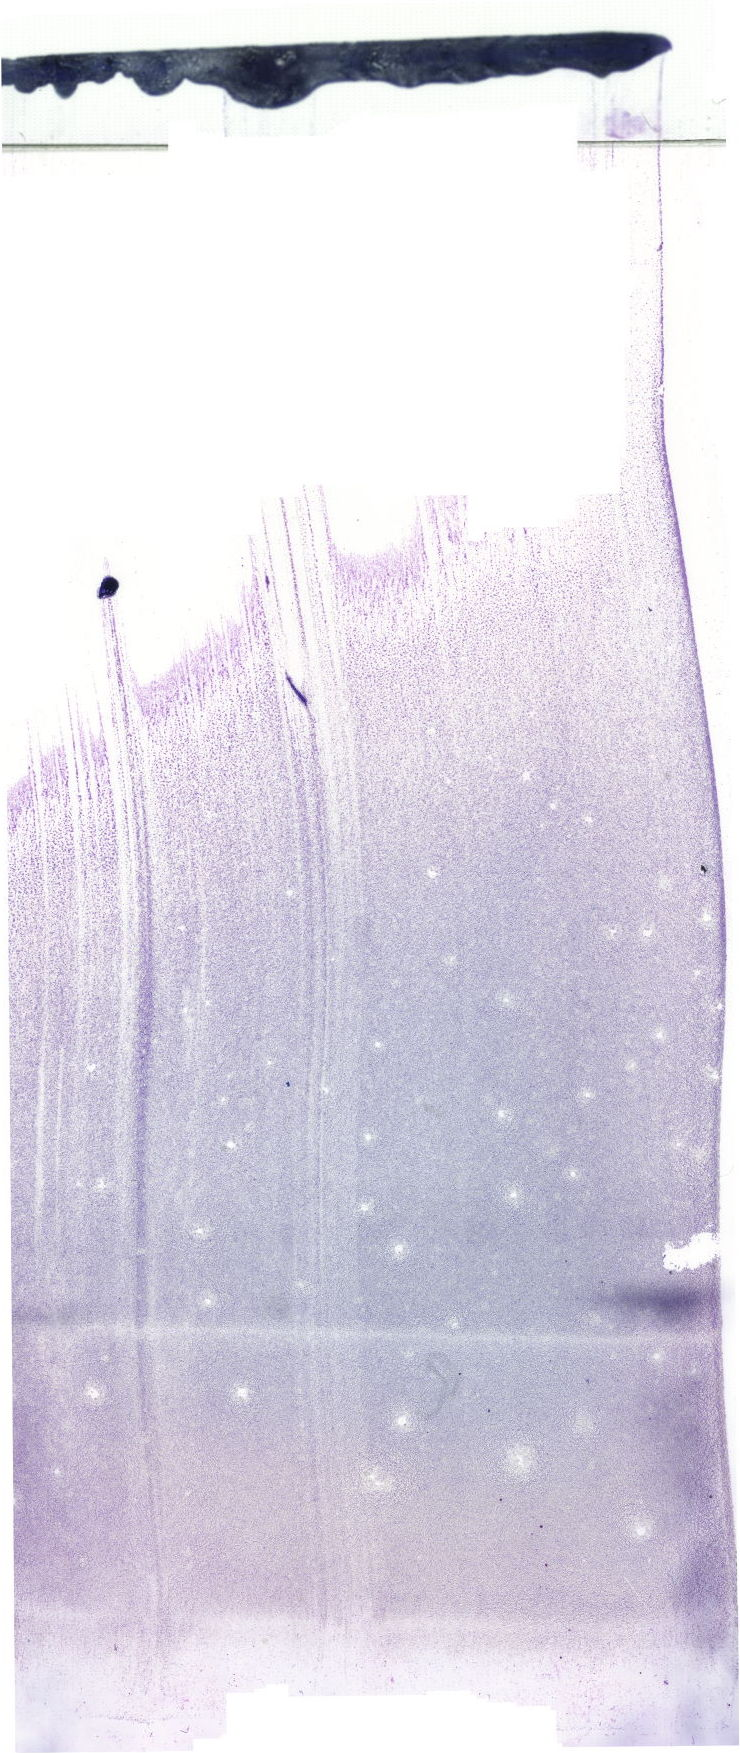
Whole-slide image of a May-Grünwald–Giemsa-stained bone marrow aspirate smear — a low-resolution overview of the entire scanned area, about 21.0 x 49.7 mm. Male patient.
Diagnosis: Chronic Phase Chronic Myeloid Leukemia, BCR-ABL1 Positive.